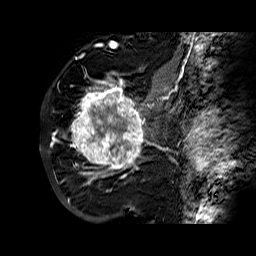
Breast MRI (dynamic contrast-enhanced), one sagittal slice; position 40 of 60 along the scan axis; dynamic contrast-enhanced series, time point 2 of 6 at this slice position (early post-contrast); 1.5 T; TE 6.3 ms, TR 32.4 ms; 256 × 256 image matrix, field of view 200 × 200 mm. Female patient. Case-level facts recorded for this patient, not image findings: setting: breast cancer imaged before/during neoadjuvant chemotherapy; receptor status: HR-positive, HER2-negative.
Annotated regions visible in this slice (semi-automatic segmentation, software-assisted and operator-edited):
- analysis volume of interest (the breast-tissue region the enhancement analysis was run in; not a lesion): bounding box [x1, y1, x2, y2] px = [68, 72, 177, 183]
- tumour enhancement mask (voxels above the 100 % enhancement threshold inside the analysis volume of interest): [71, 73, 172, 183]